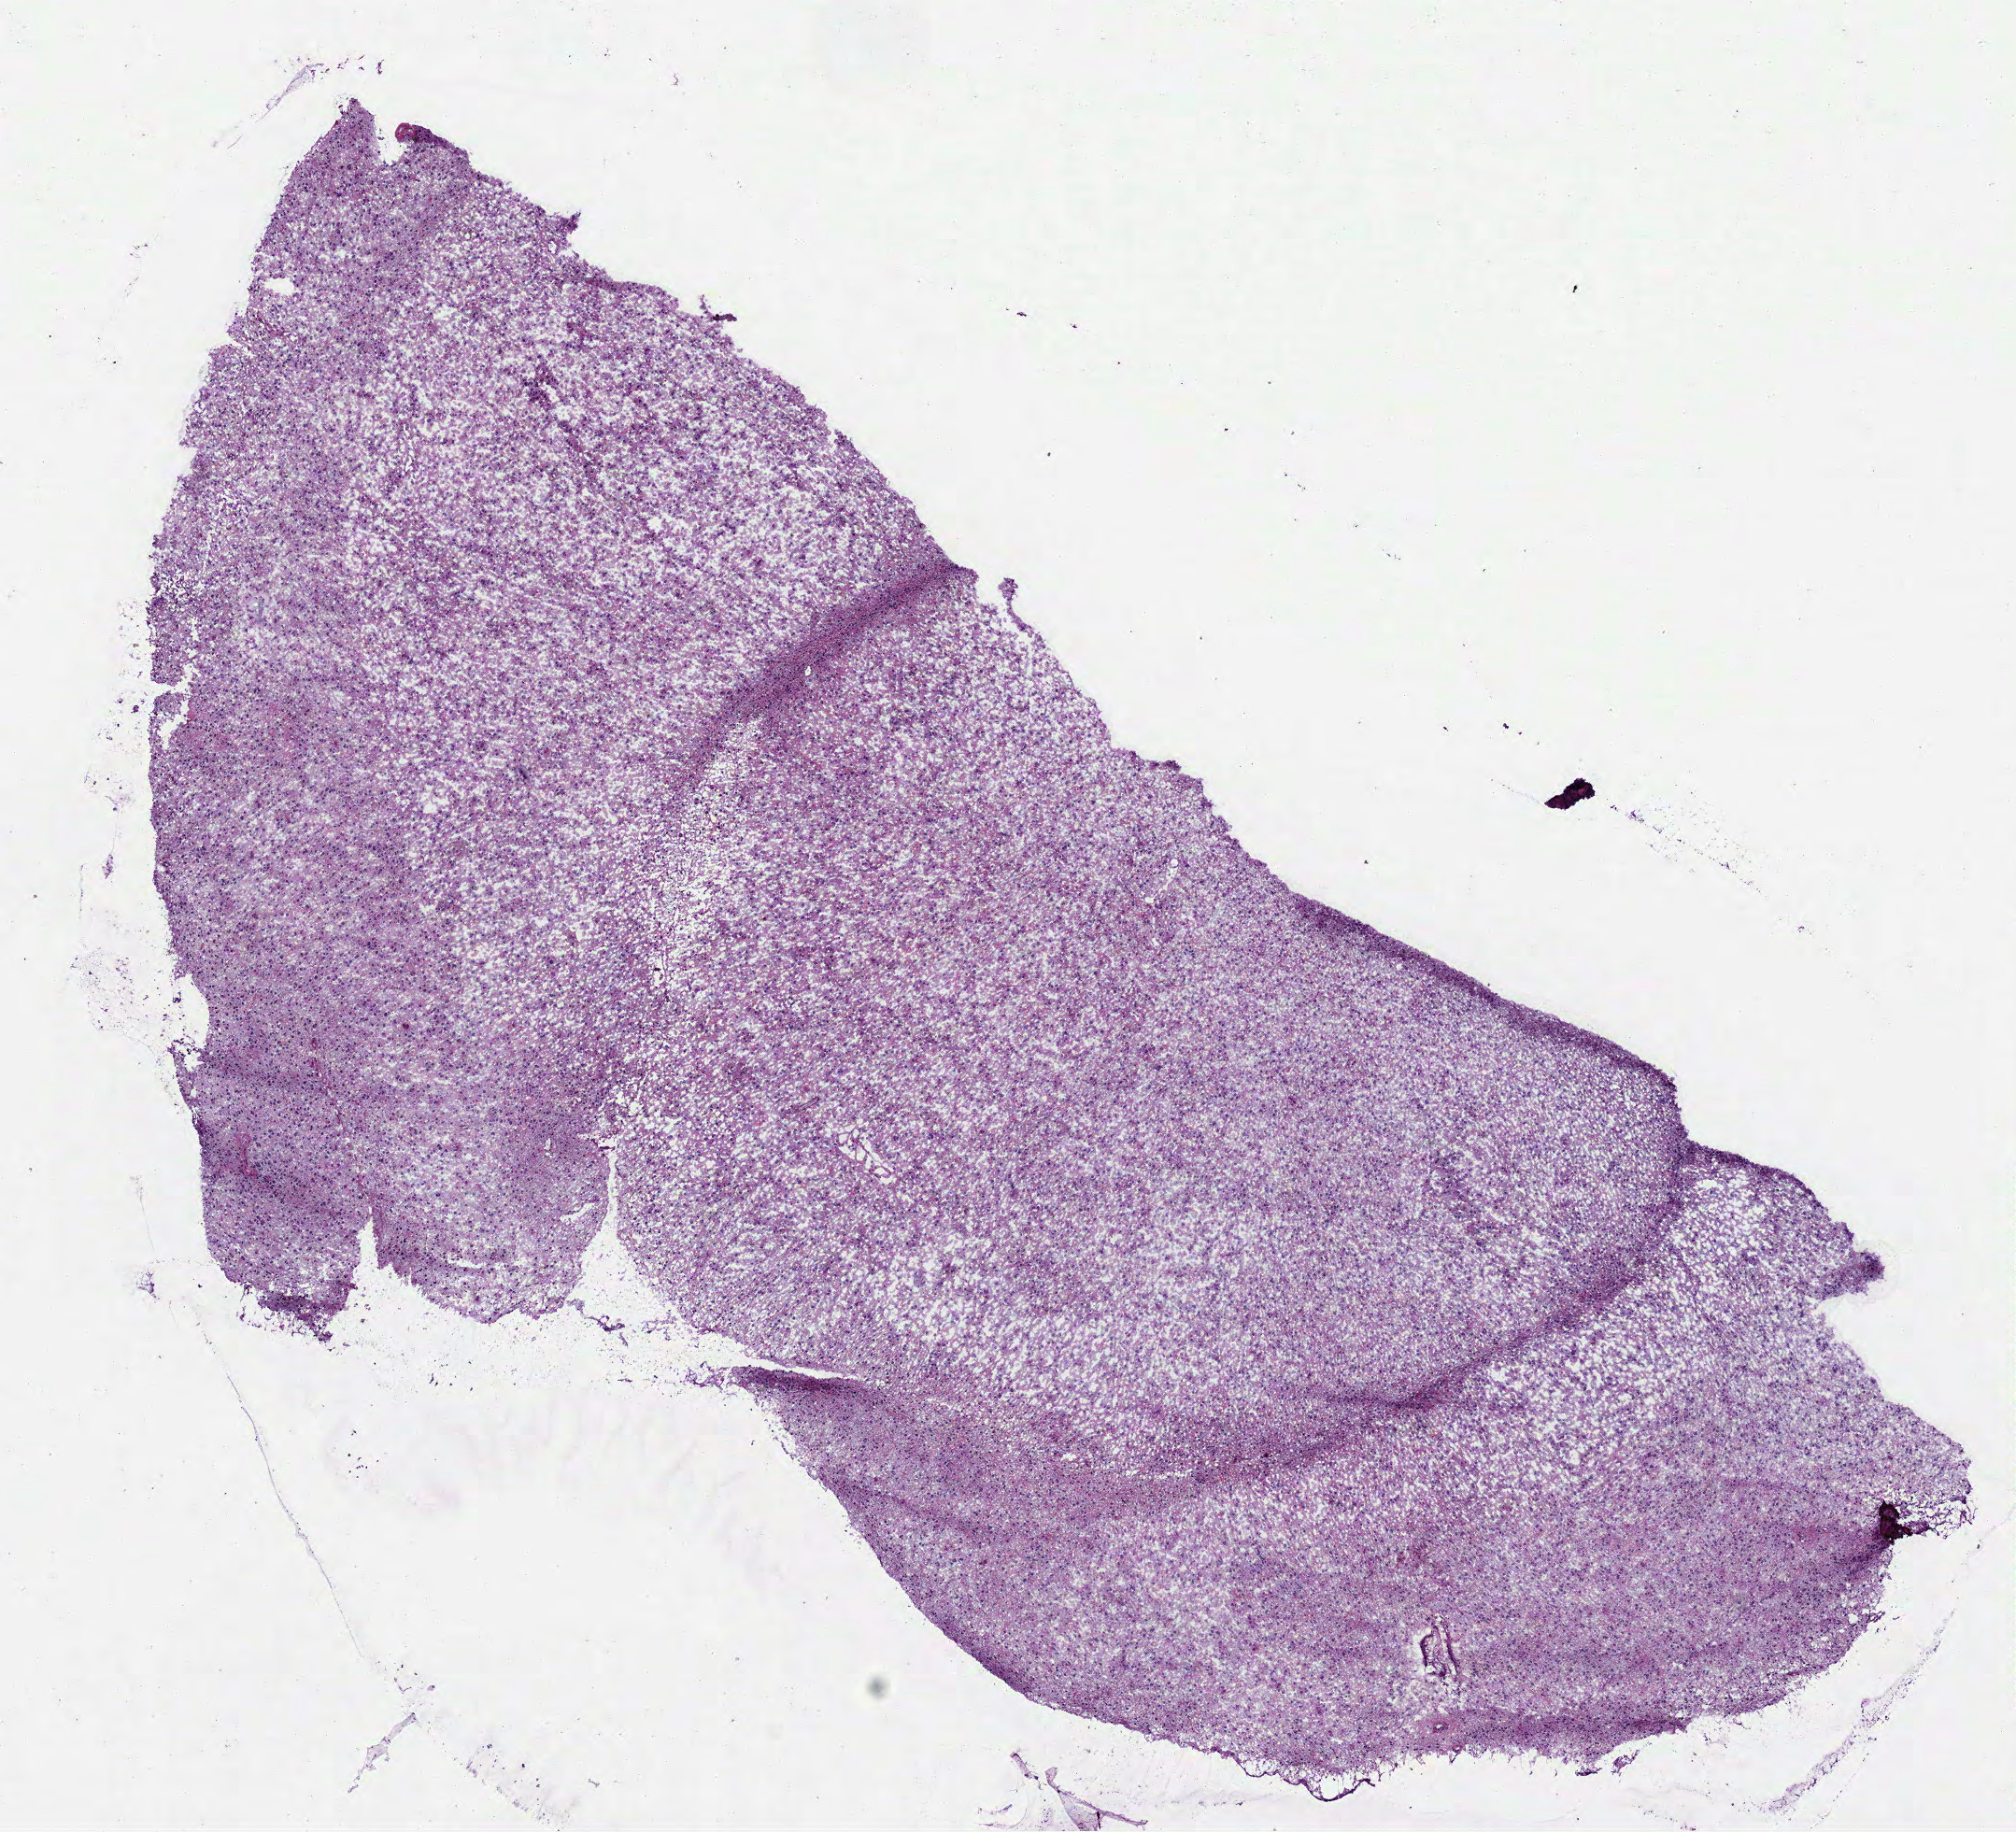
H&E-stained whole-slide image, low-resolution overview of the scanned area, about 8.7 x 7.9 mm; frozen section; sample: primary tumour, brain. Male, age 31 years at initial diagnosis. Histologic grade: G3 (poorly differentiated). Pathologist review of this section (percent, as recorded): tumour cells 100%, tumour nuclei 75%, normal cells 0%, stromal cells 0%, necrosis 0%.
Diagnosis: Mixed glioma (cerebrum).